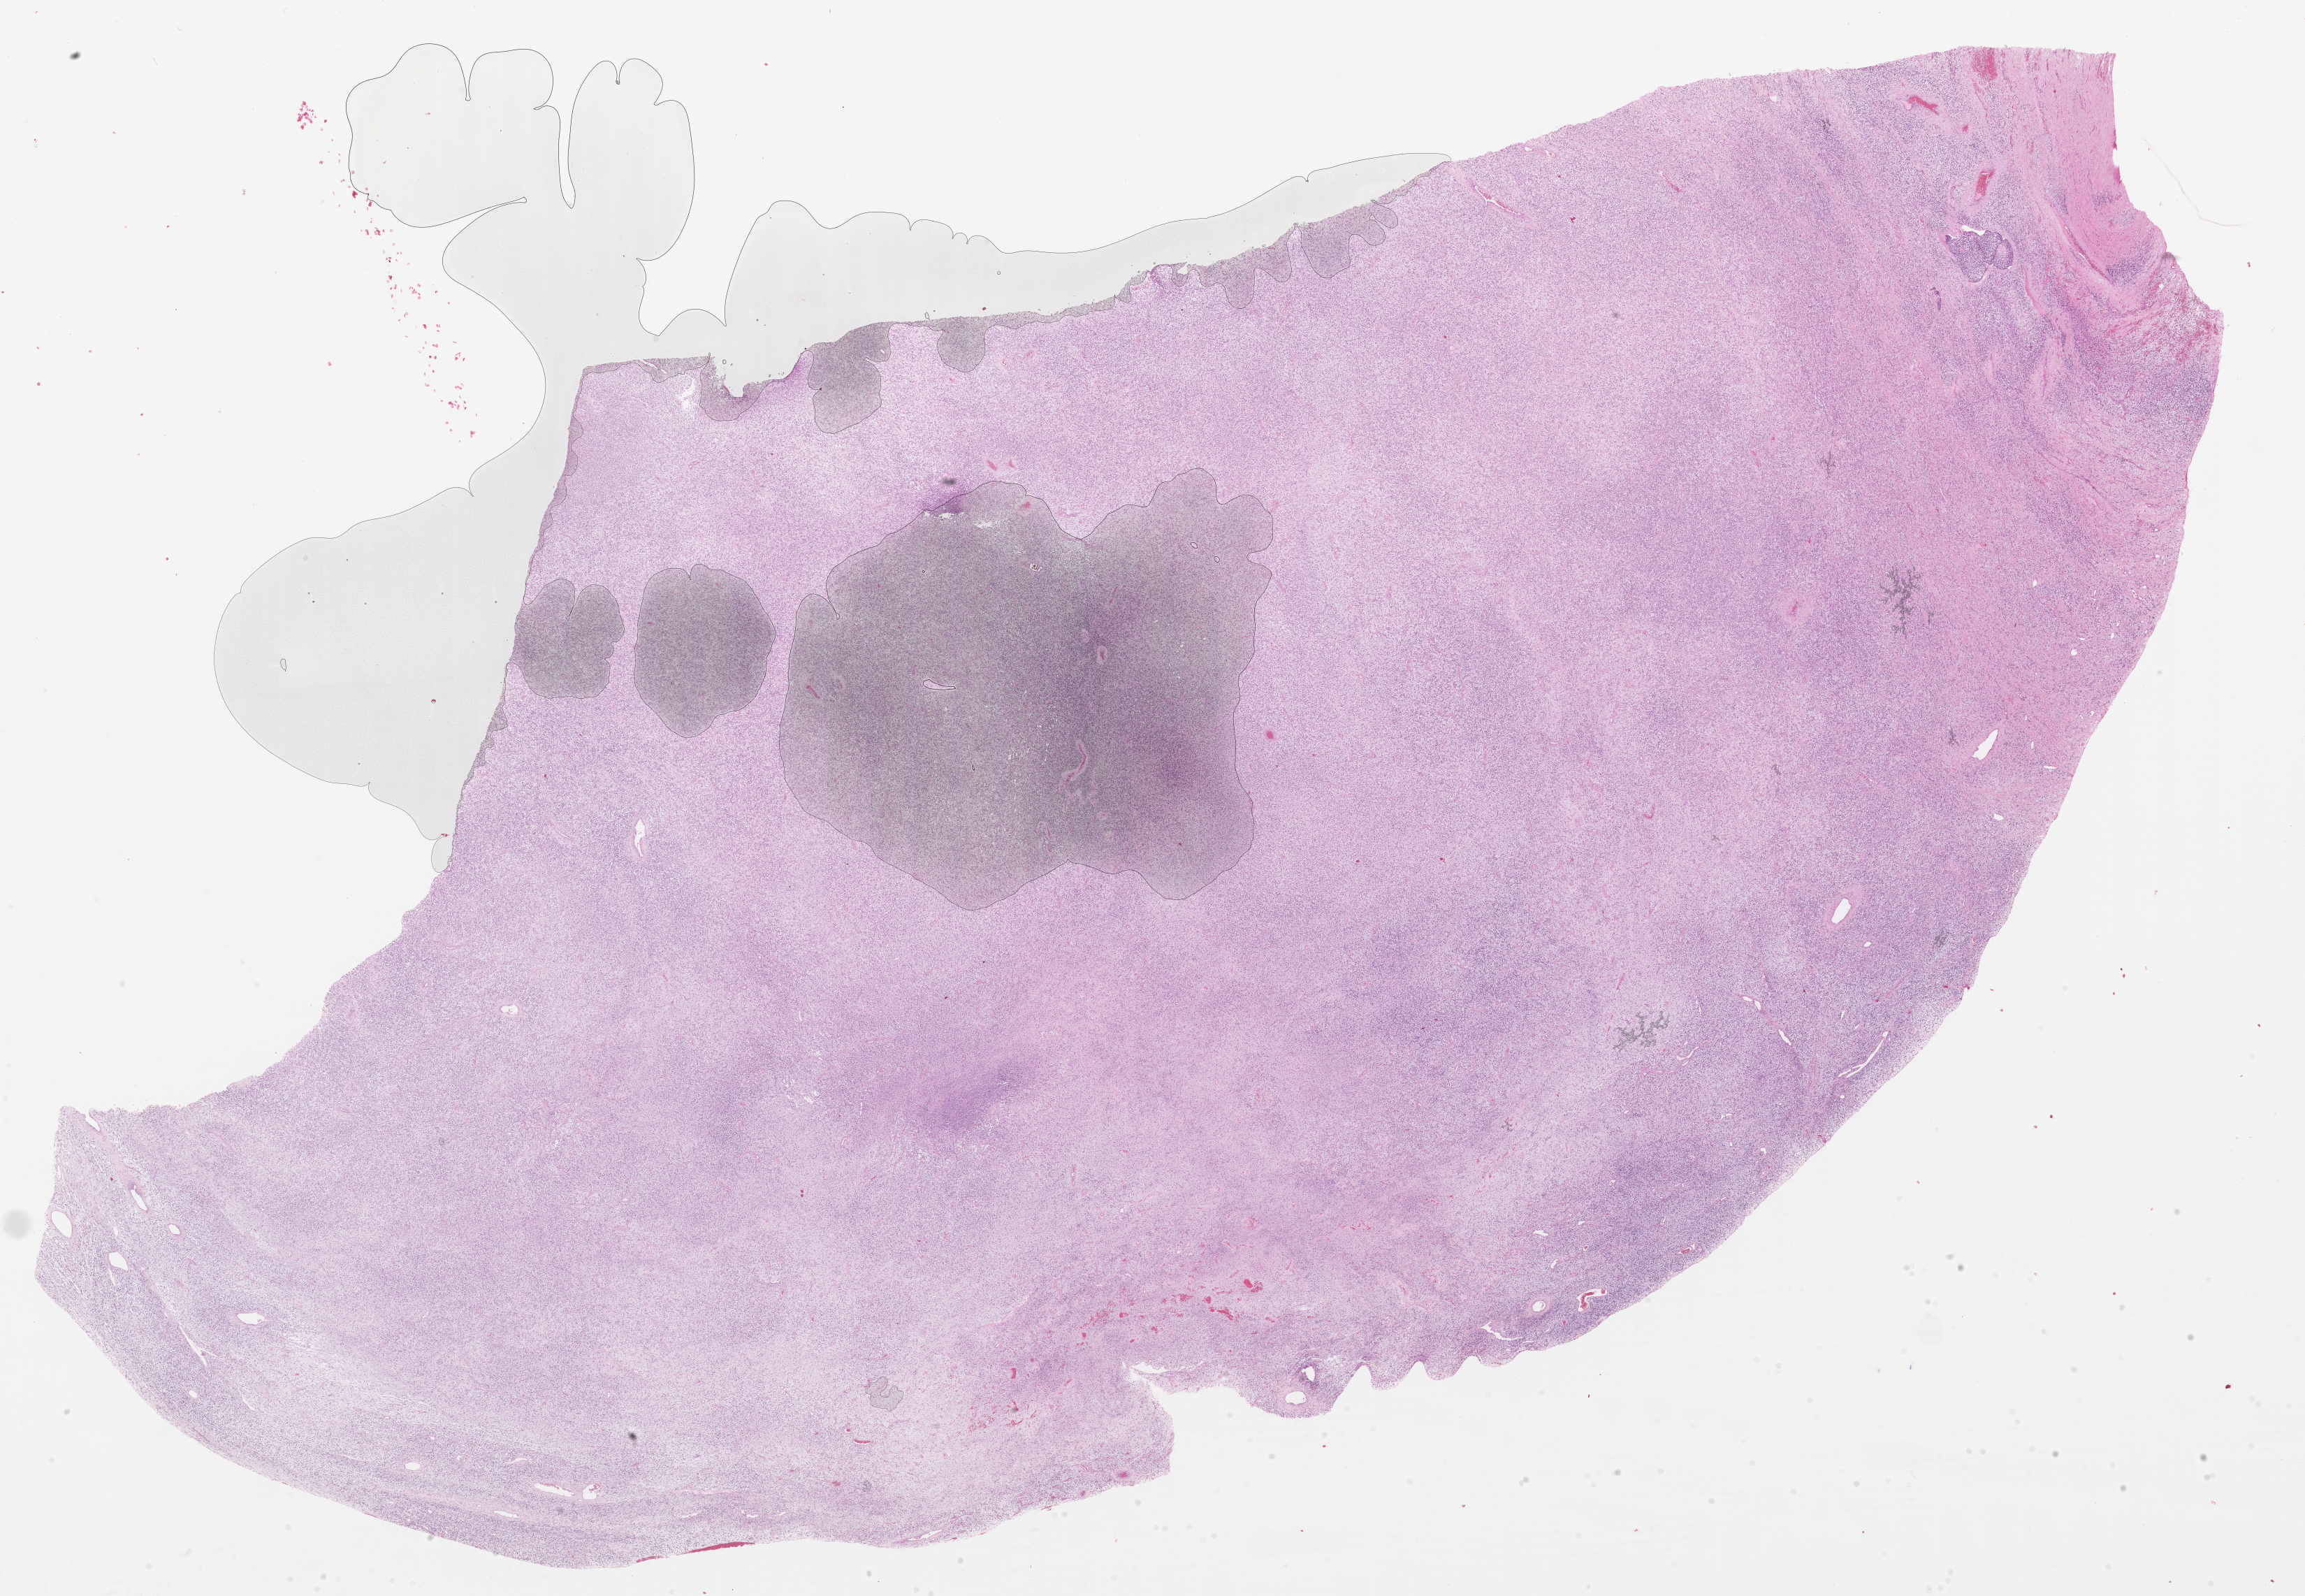
Whole-slide image, H&E stain of tumor tissue — whole scanned area (about 26.7 x 18.5 mm) shown as a low-resolution overview, FFPE section, site: testicle, right. Patient: male, age 14.5 years at diagnosis.
Primary site (case record): testis-Paratestis. Diagnosis: rhabdomyosarcoma; histological classification: embryonal rhabdomyosarcoma. Stage (as recorded): 4.